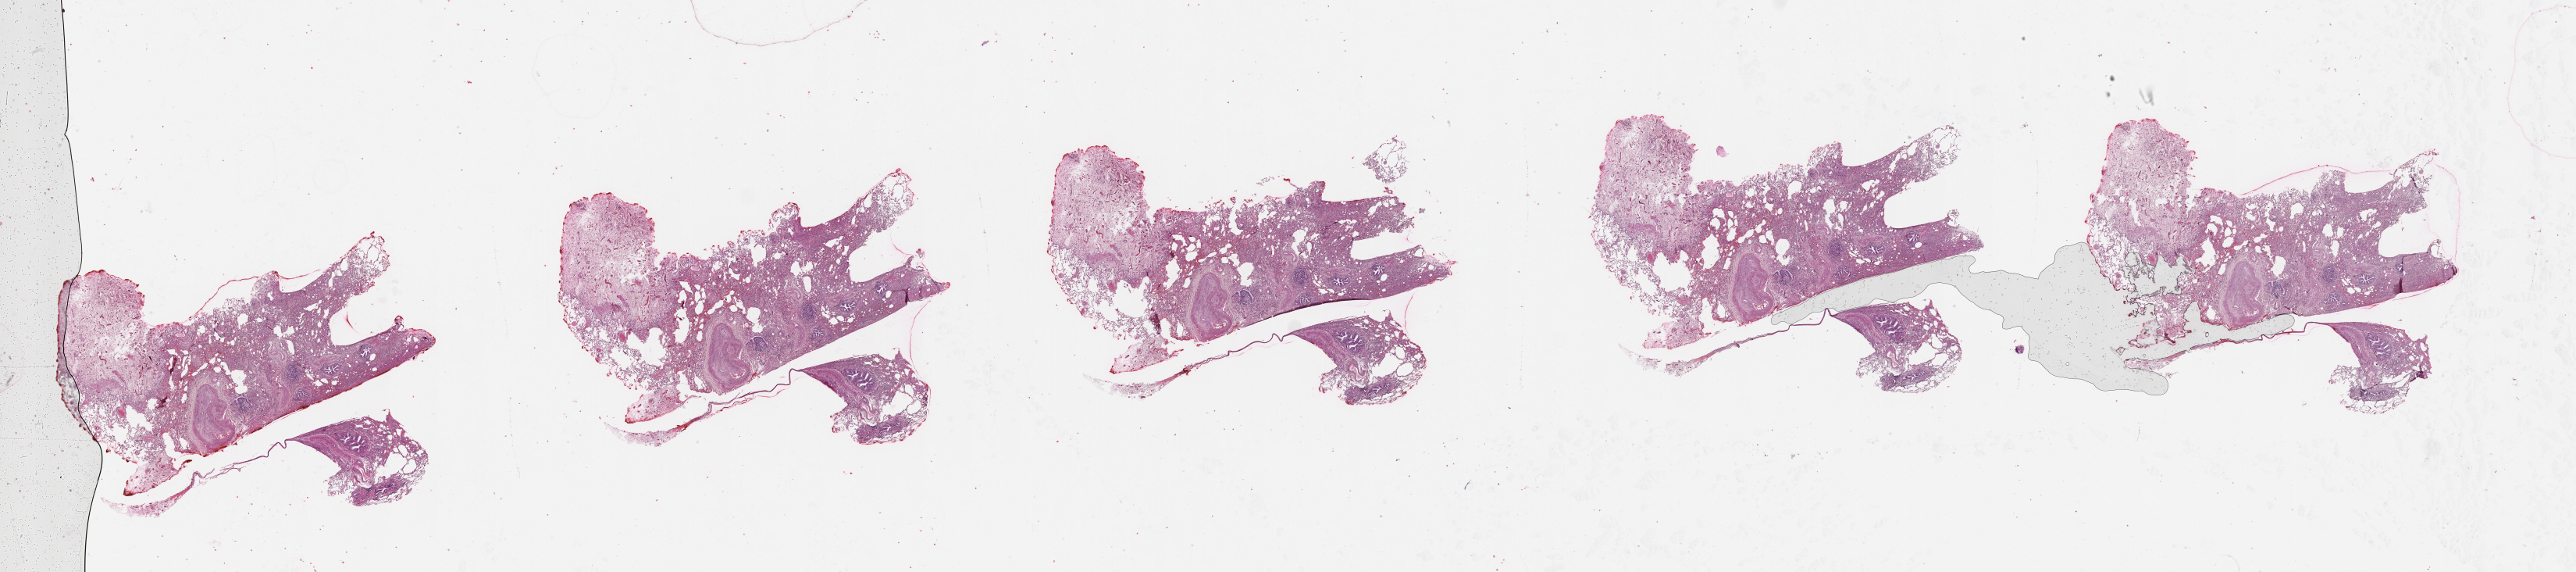
Whole-slide histology image, Hematoxylin and eosin (H&E) stained, shown as a low-resolution overview of the whole scanned area (about 53.1 x 11.8 mm, from a 20x scan). Lung, tissue type not recorded.
Patient diagnosis (cohort enrolment): lung adenocarcinoma (lung).